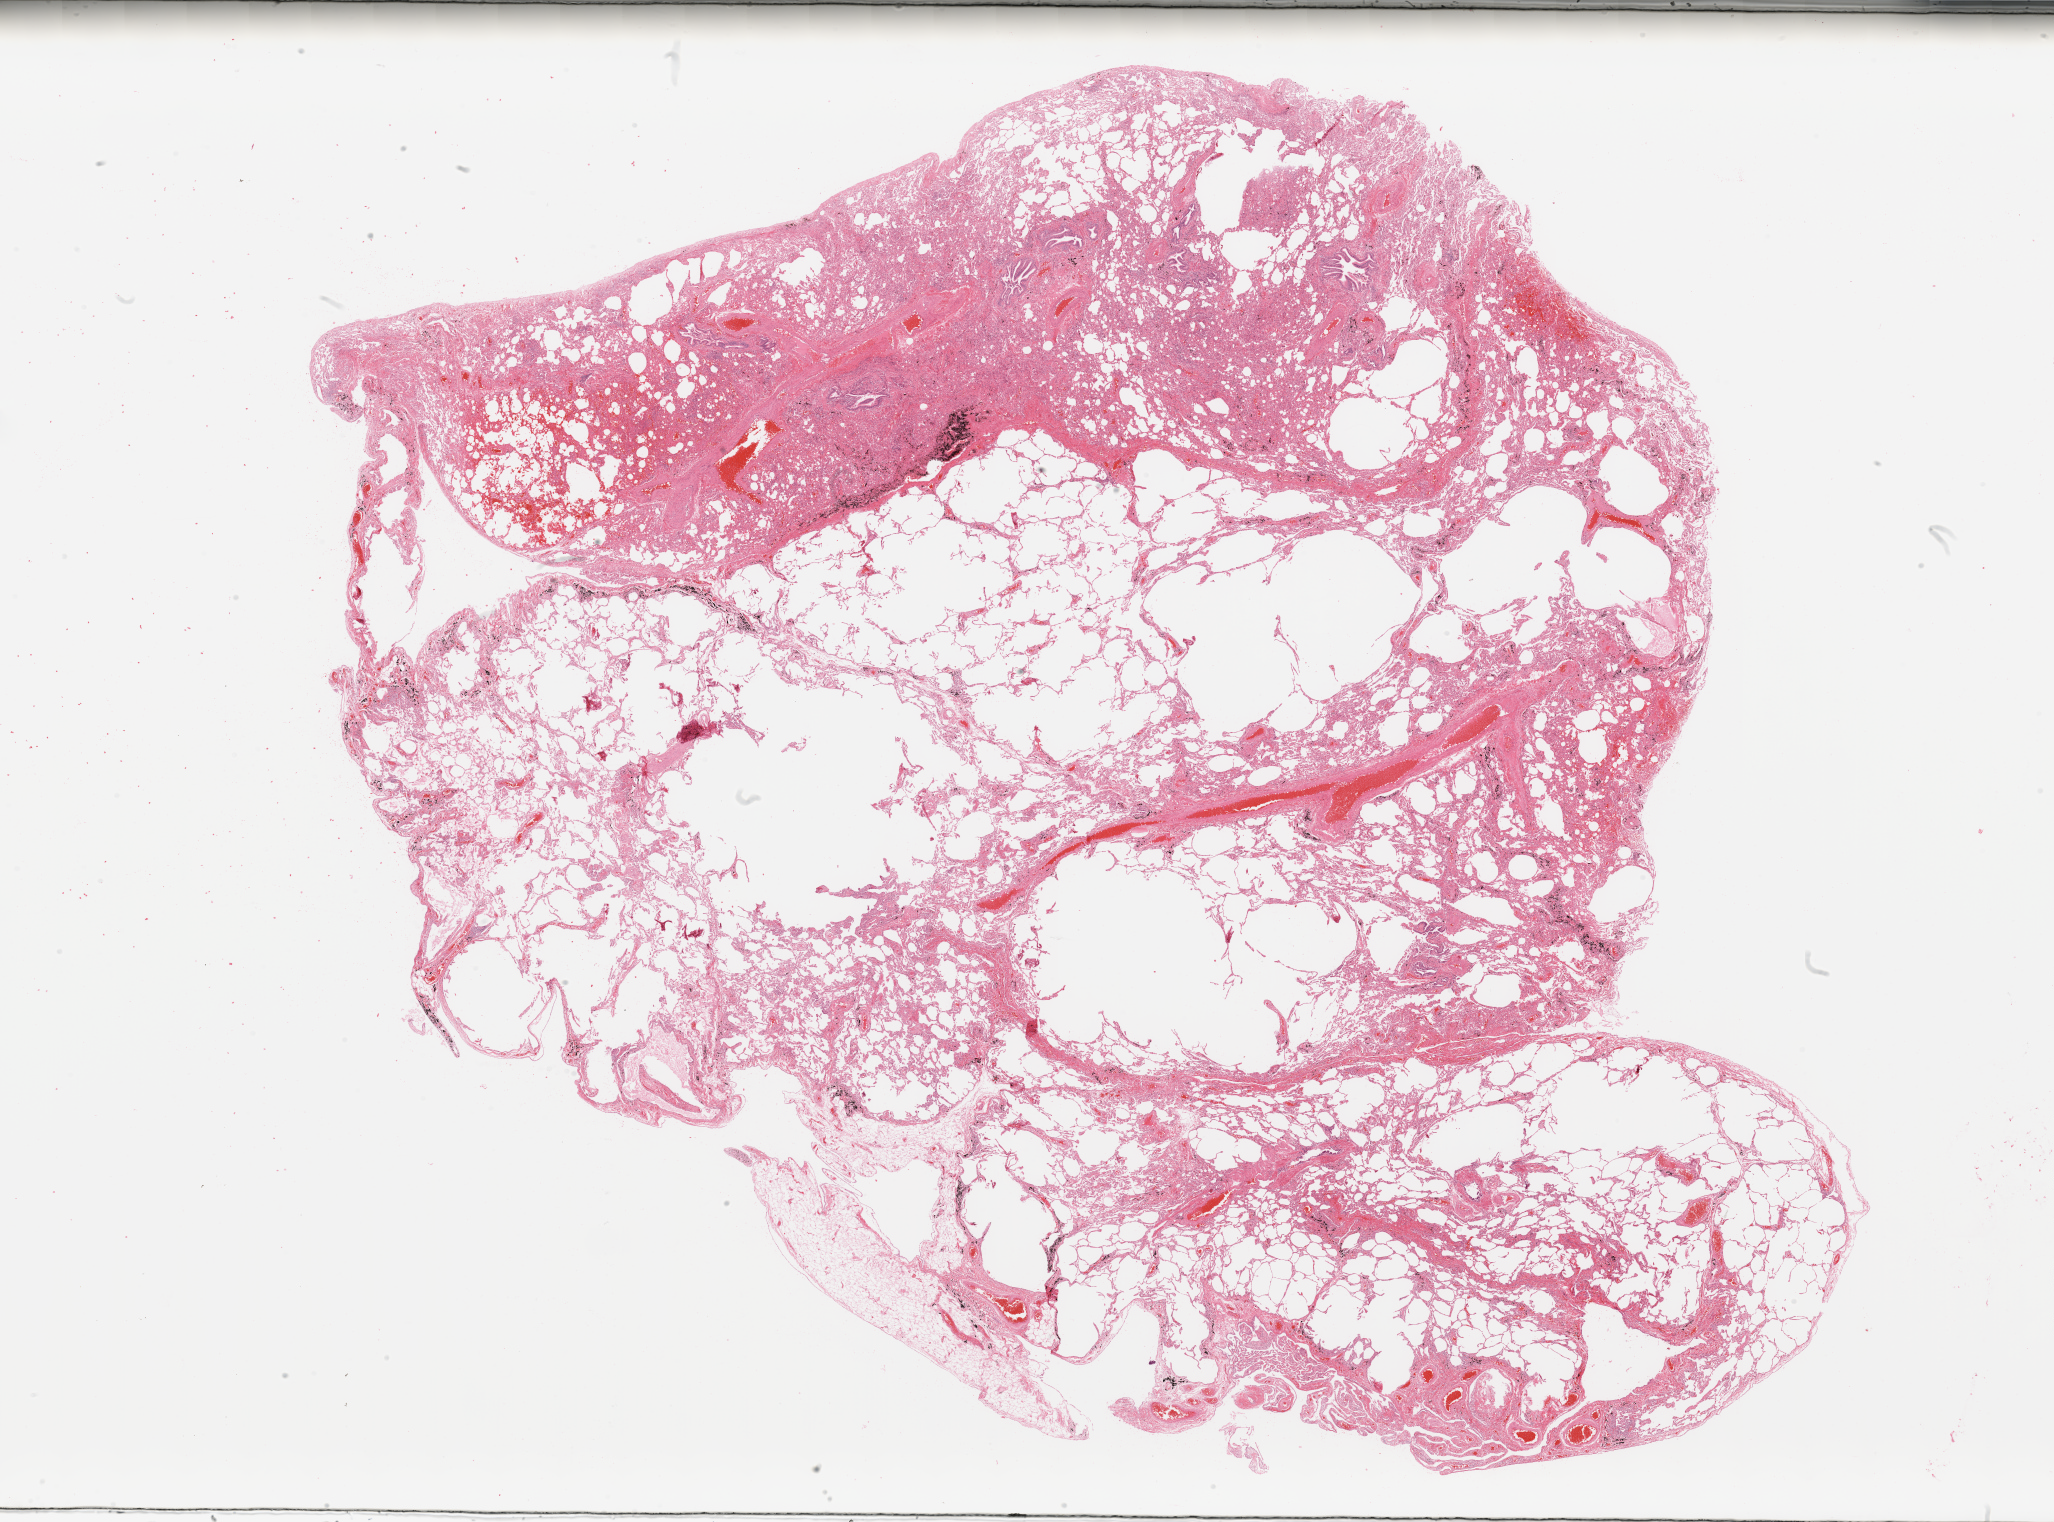
H&E whole-slide image — whole scanned area (about 32.5 x 24.1 mm) shown as a low-resolution overview. Normal (non-tumour) tissue sample, sampled site: lung. Patient: male, age 69 years.
This section: normal (non-tumour) tissue from the same patient. Patient diagnosis: Adenocarcinoma, NOS.